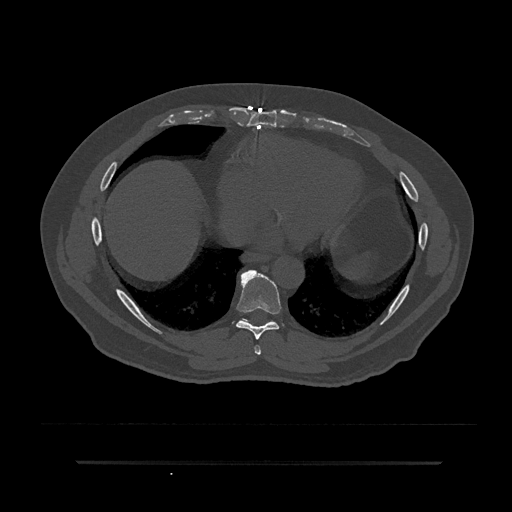
CT including the spine, one axial slice. Slice 419 of 797 in the series (ordered by position). Reconstruction kernel Br40s/3. 120 kVp. Bone window (W 1800 / L 400 HU). 512 × 512 image matrix, field of view 464 × 464 mm. Patient: male, 59 years. From the clinical record (not read from this slice): primary cancer: bile ducts.
Outlined on this slice (semi-automatic segmentation, software-assisted and operator-edited):
- T7 vertebra: bounding box (x1, y1, x2, y2) in pixels: (254, 345, 261, 355)
- T8 vertebra: (236, 270, 281, 340)